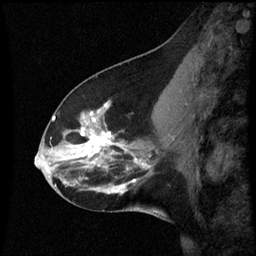
Breast MRI (dynamic contrast-enhanced), one sagittal slice. Position 26 of 60 along the scan axis. Dynamic contrast-enhanced series, image 2 of 3 at this slice position (ordered by acquisition). 1.5 T. TE 4.2 ms, TR 8.9 ms. 2 mm slice thickness. 256 × 256 image matrix, field of view 200 × 200 mm. Female patient, age 45 years. From the clinical record (not read from this slice): setting: breast cancer imaged before/during neoadjuvant chemotherapy; receptor status: HR-positive, HER2-negative.
Structures marked on this image (semi-automatic segmentation, software-assisted and operator-edited):
- analysis volume of interest (the breast-tissue region the enhancement analysis was run in; not a lesion): box from (x=46, y=94) to (x=171, y=205) px
- tumour enhancement mask (voxels above the 70 % enhancement threshold inside the analysis volume of interest): (x=52, y=104)–(x=143, y=183)